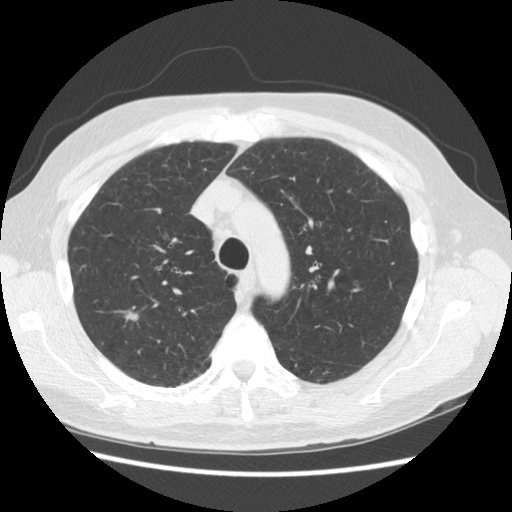
Chest CT (low-dose screening protocol), one axial image, third annual screen, lung window (W 1500 / L -600 HU), 2.5 mm slice thickness, standard (soft-tissue) reconstruction kernel (STANDARD), slice 116 of 156 in the series. Male, age 68 years at enrolment. Current smoker at enrolment.
Expert-annotated lung lesion, box from (x=102, y=298) to (x=153, y=343) px. The exam's reader record, not a measurement of the box and not confirmed to be the same lesion: non-calcified nodule or mass ≥4 mm, right upper lobe, 11 × 9 mm, smooth margins, soft tissue attenuation, pre-existing on the prior screen: yes; interval growth: yes. Official screen result: positive, other. Later outcome: lung cancer diagnosed 246 days after this screen — adenocarcinoma, NOS, right upper lobe, moderately differentiated (G2), stage IA (AJCC 6th edition), 13 mm at pathology.